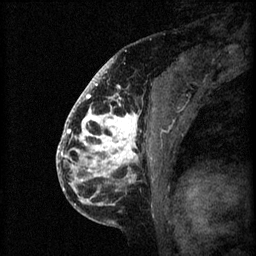
Breast MRI (dynamic contrast-enhanced), one sagittal slice. Position 37 of 60 along the scan axis. 3 images stored at this slice position (order not interpretable as contrast timing). 1.5 T. TE 4.2 ms, TR 8.2 ms. 2 mm slice thickness. 256 × 256 image matrix, field of view 180 × 180 mm. Patient: female, 41 years.
Outlined on this slice (semi-automatically segmented with operator editing):
- analysis volume of interest (the breast-tissue region the enhancement analysis was run in; not a lesion): bounding box (x1, y1, x2, y2) in pixels: (72, 108, 158, 205)
- tumour enhancement mask (voxels above the 70 % enhancement threshold inside the analysis volume of interest): (72, 108, 139, 203)